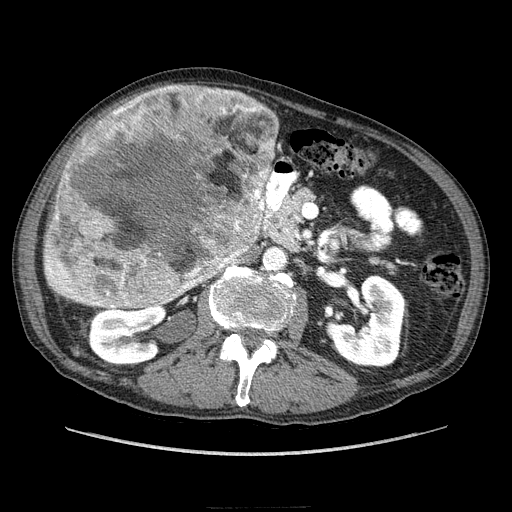
Contrast-enhanced abdominal CT (liver protocol), one axial slice. Slice 103 of 218 in the series (ordered by position). Soft-tissue window (W 400 / L 40 HU). 512 × 512 image matrix, field of view 380 × 380 mm. From the clinical record (not read from this slice): diagnosis: hepatocellular carcinoma (patient treated with transarterial chemoembolisation; whether this scan precedes or follows treatment is not stated here); TNM stage (as recorded): Stage-IIIA; Child-Pugh class: A; tumour differentiation: well differentiated; tumour size: 20 cm.
Annotated regions visible in this slice (semi-automatic segmentation, software-assisted and operator-edited):
- mass: box from (x=40, y=84) to (x=276, y=311) px